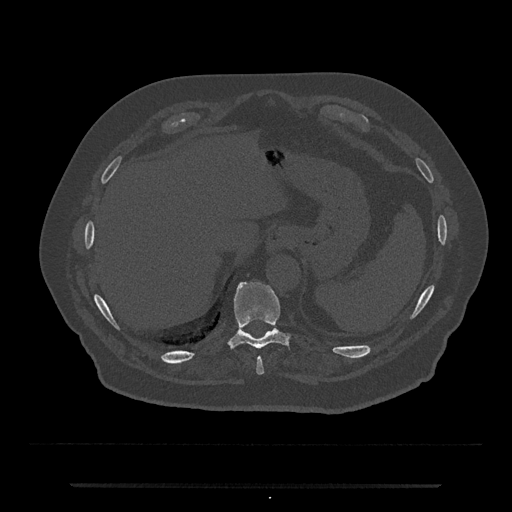
CT including the spine, one axial slice; slice 707 of 797 in the series (ordered by position); 120 kVp; bone window (W 1800 / L 400 HU); 0.5 mm slice thickness; 512 × 512 image matrix, field of view 434 × 434 mm. Patient: male, 80 years. Case-level facts recorded for this patient, not image findings: primary cancer: prostate; vertebrae with lytic lesions (as recorded): L1, T11.
Structures marked on this image (semi-automatic segmentation, software-assisted and operator-edited):
- T10 vertebra: bounding box (x1, y1, x2, y2) in pixels: (229, 281, 289, 349)
- T9 vertebra: (256, 357, 264, 375)